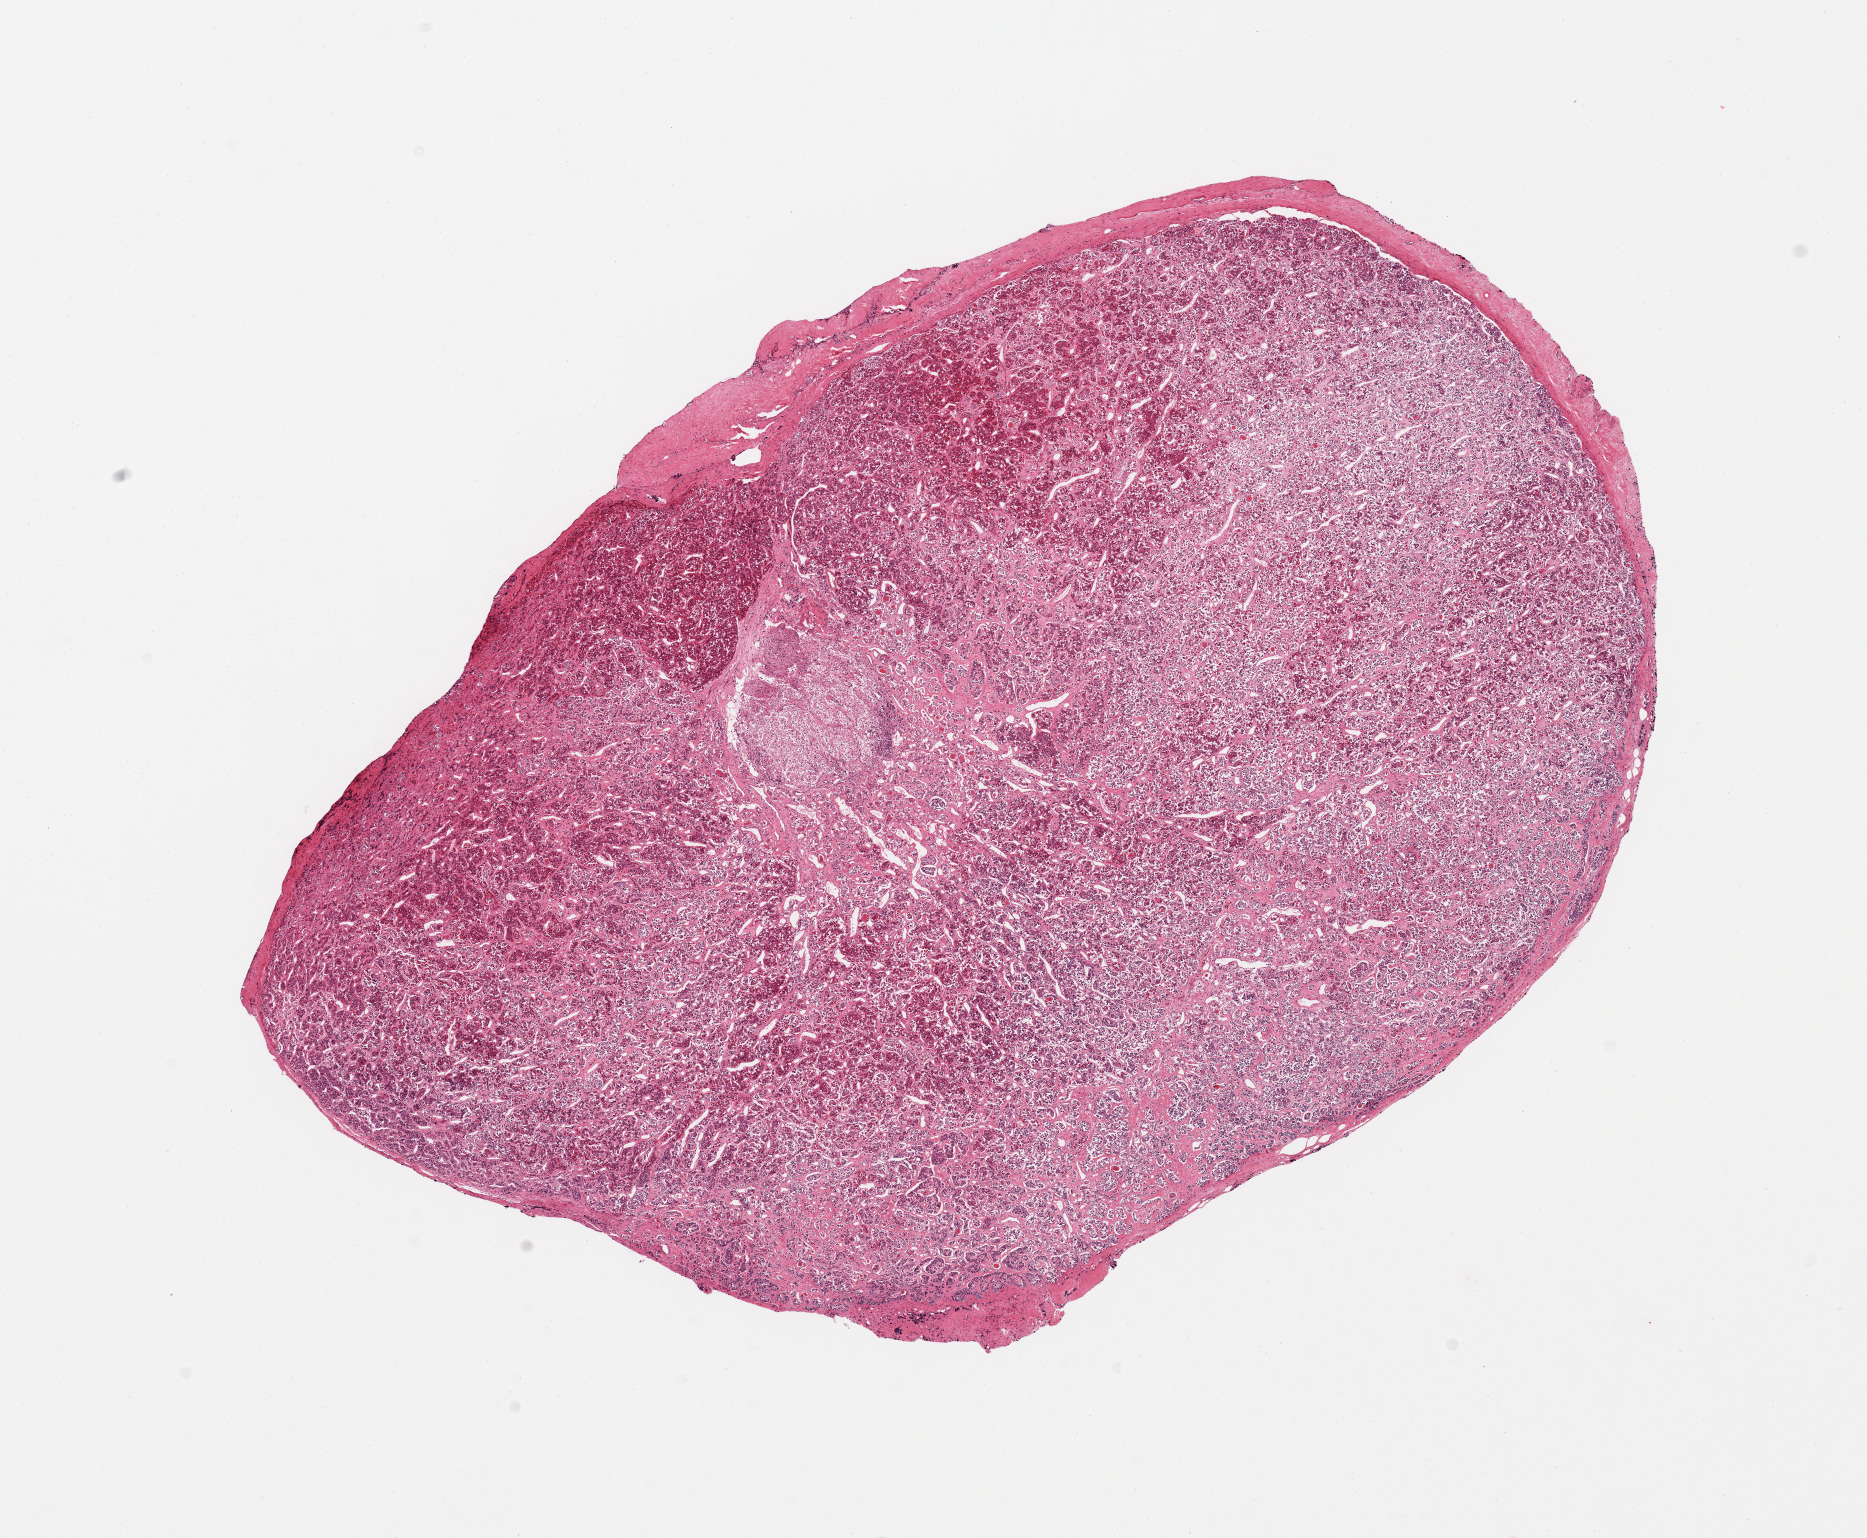
Digitized hematoxylin and eosin (H&E)-stained section — low-resolution overview of the scanned area, about 14.8 x 12.2 mm (acquisition: 20x scan). PAXgene-fixed, paraffin-embedded tissue. Target tissue: pituitary. Tissue donor sample. Male donor.
Review note (as recorded): 1 piece, adenohypophysis; minute focus (~1mm) neurohypophysis noted.